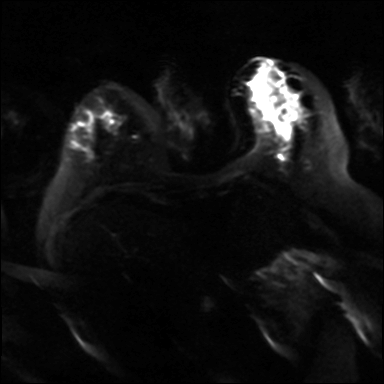
Breast MRI, one axial slice; position 8 of 36 along the scan axis; diffusion-weighted series; image 2 of 4 stored at this slice position (different b-values; order by instance number); 3 T; 4 mm slice thickness; 384 × 384 image matrix, field of view 320 × 320 mm. Female patient.
Outlined on this slice (expert manual segmentation):
- tumour on diffusion-weighted imaging: bounding box [x1, y1, x2, y2] px = [262, 108, 298, 117]